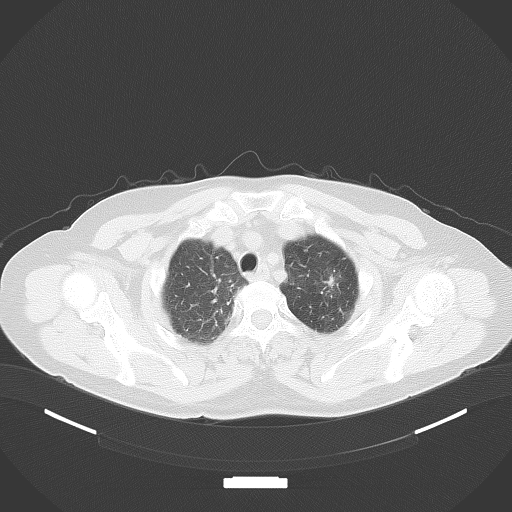
Chest CT, one axial slice; slice 73 of 116 in the series (ordered by position); lung window (W 1500 / L -600 HU); 3 mm slice thickness; 512 × 512 image matrix. Female patient, age 64 years. From the clinical record (not read from this slice): clinical TNM (as recorded): T1c N0 M0.
Annotated regions visible in this slice (bounding box drawn by a radiologist):
- lung tumour (recorded histology: adenocarcinoma): bounding box [x1, y1, x2, y2] px = [325, 270, 338, 297]